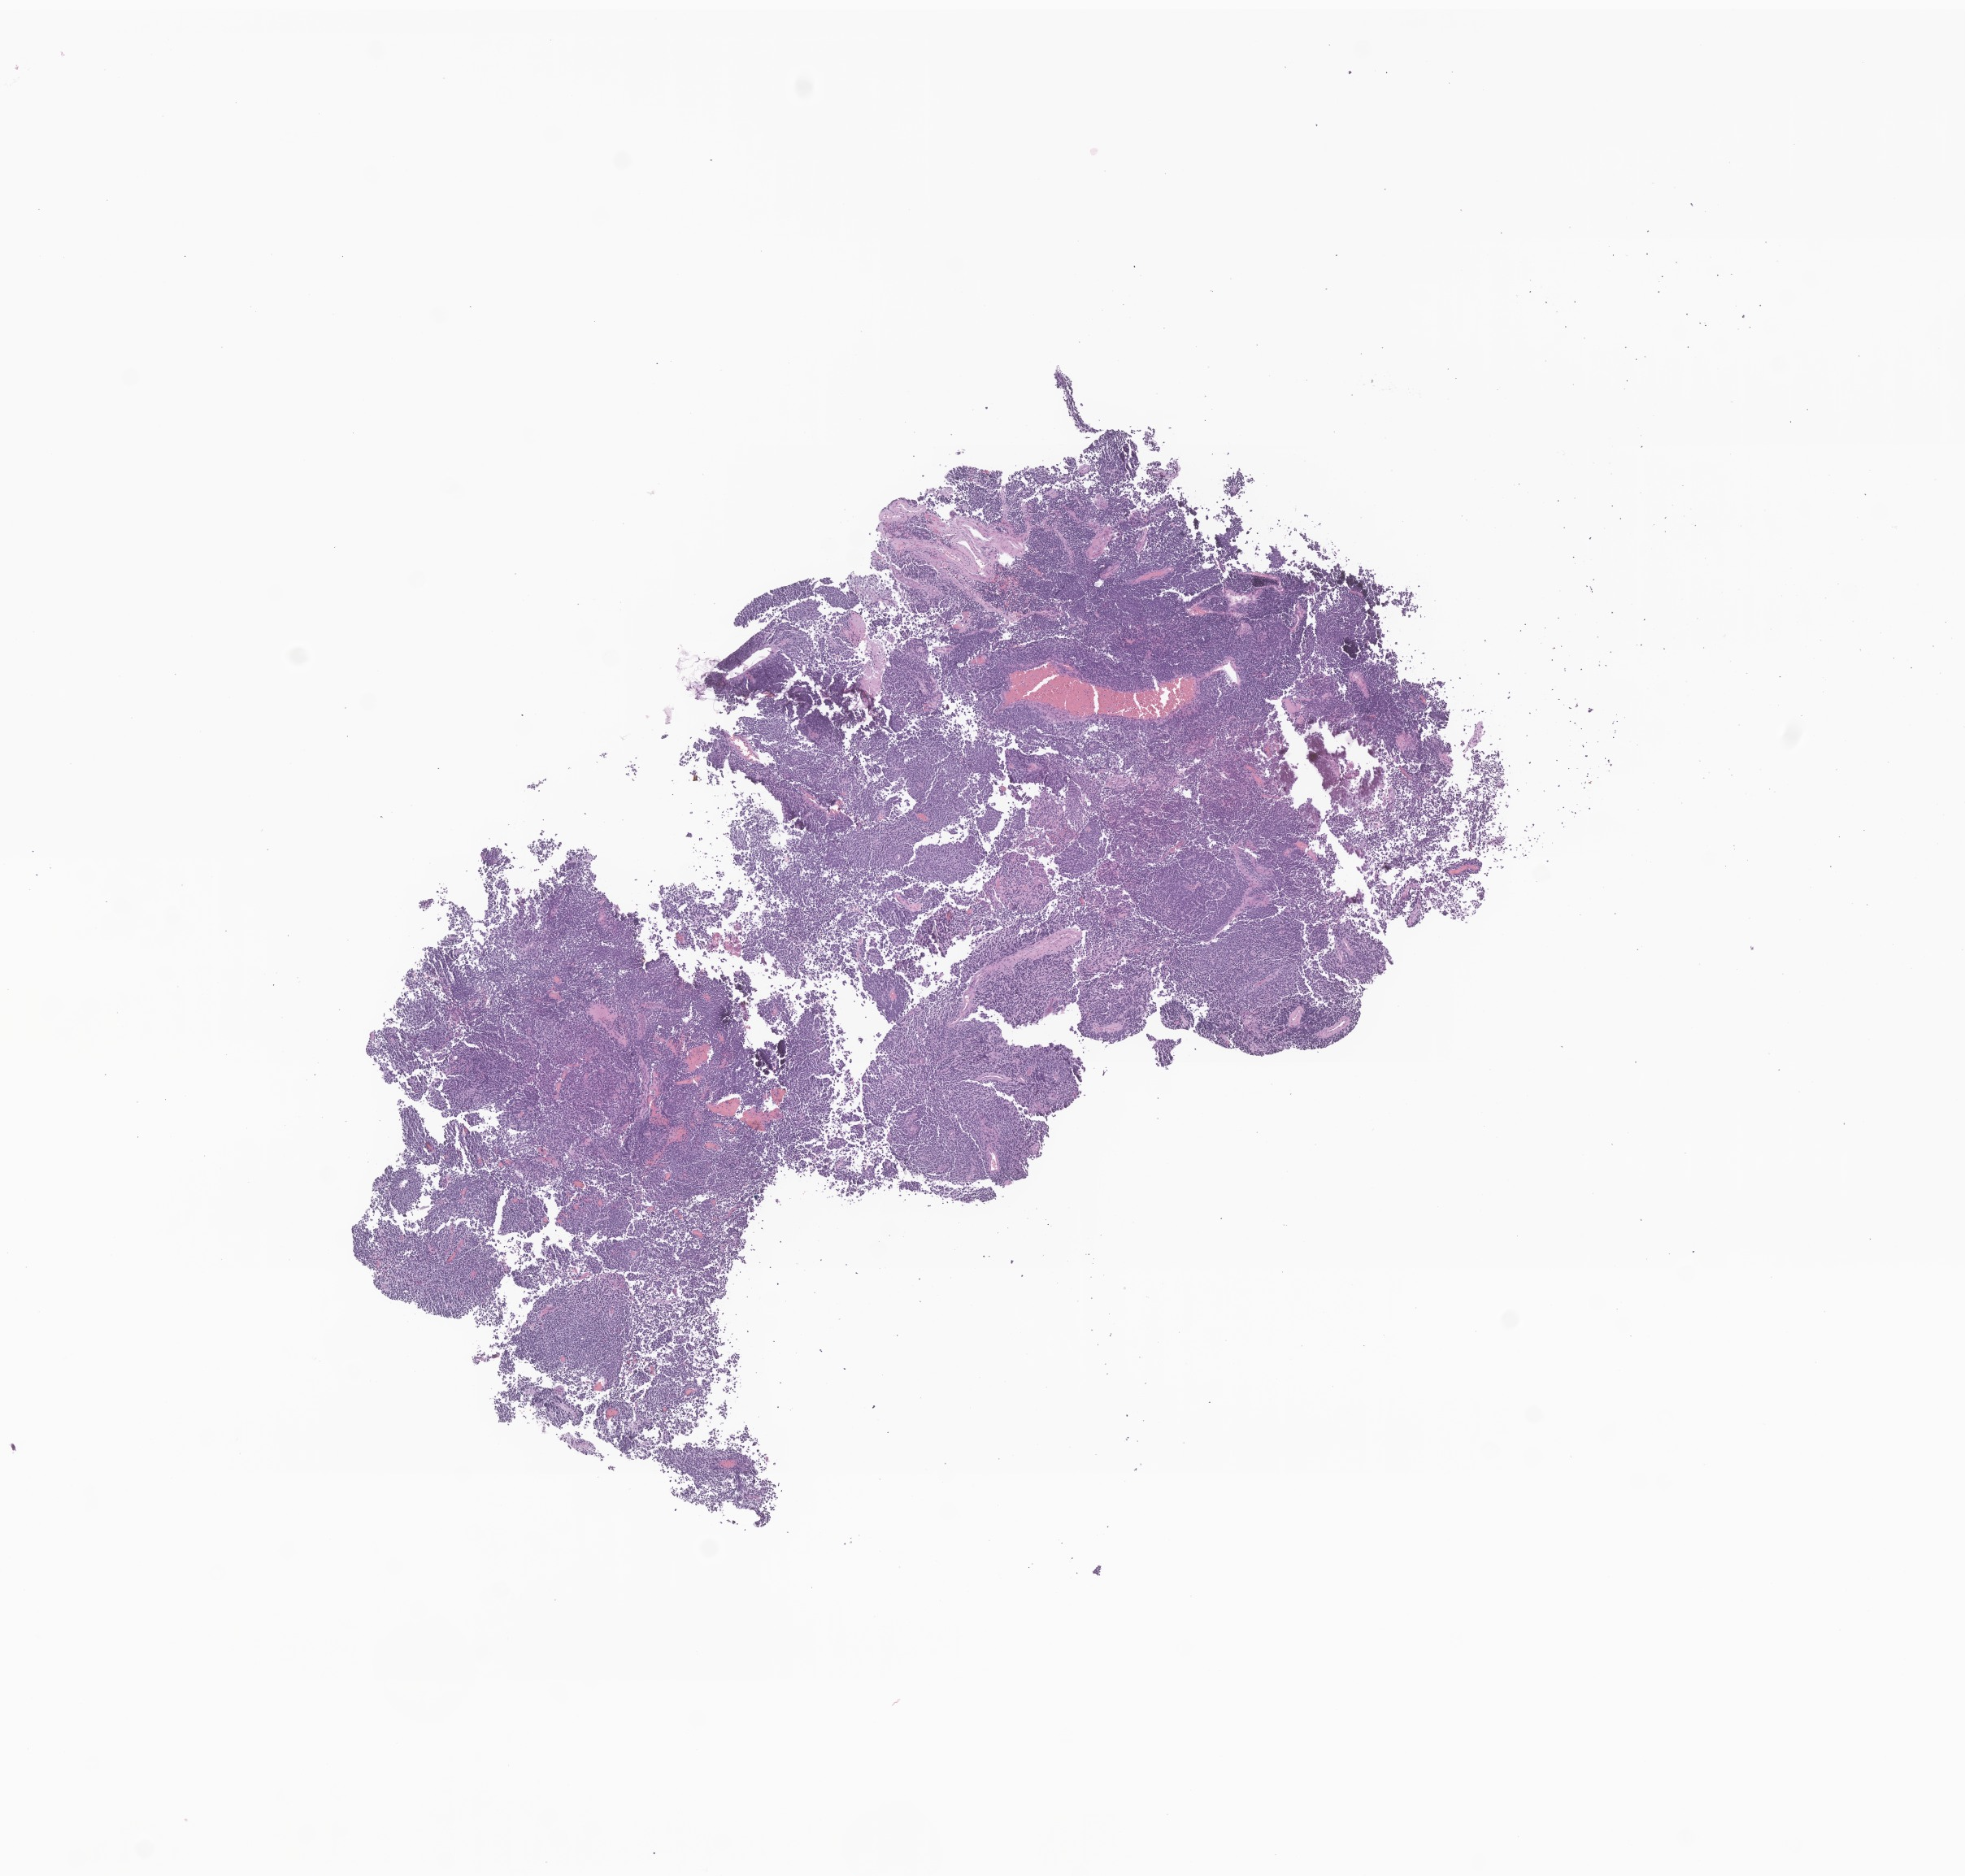
H&E whole-slide image of tumor tissue from the brain — whole scanned area (about 10.2 x 9.7 mm) shown as a low-resolution overview. FFPE section. Patient: female, age 172 months (14 years 4 months).
- diagnosis: Pineoblastoma